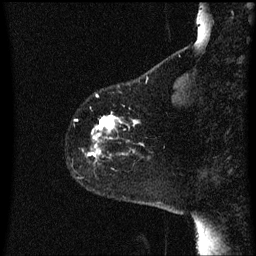
Breast MRI (dynamic contrast-enhanced), one sagittal slice; dynamic contrast-enhanced series, image 2 of 3 at this slice position (ordered by acquisition); 1.5 T; TE 4.2 ms, TR 8 ms; 256 × 256 image matrix, field of view 200 × 200 mm. Patient: female, 60 years.
Annotated regions visible in this slice (semi-automatically segmented with operator editing):
- analysis volume of interest (the breast-tissue region the enhancement analysis was run in; not a lesion): bounding box (x1, y1, x2, y2) in pixels: (77, 112, 144, 165)
- tumour enhancement mask (voxels above the 70 % enhancement threshold inside the analysis volume of interest): (89, 116, 140, 157)